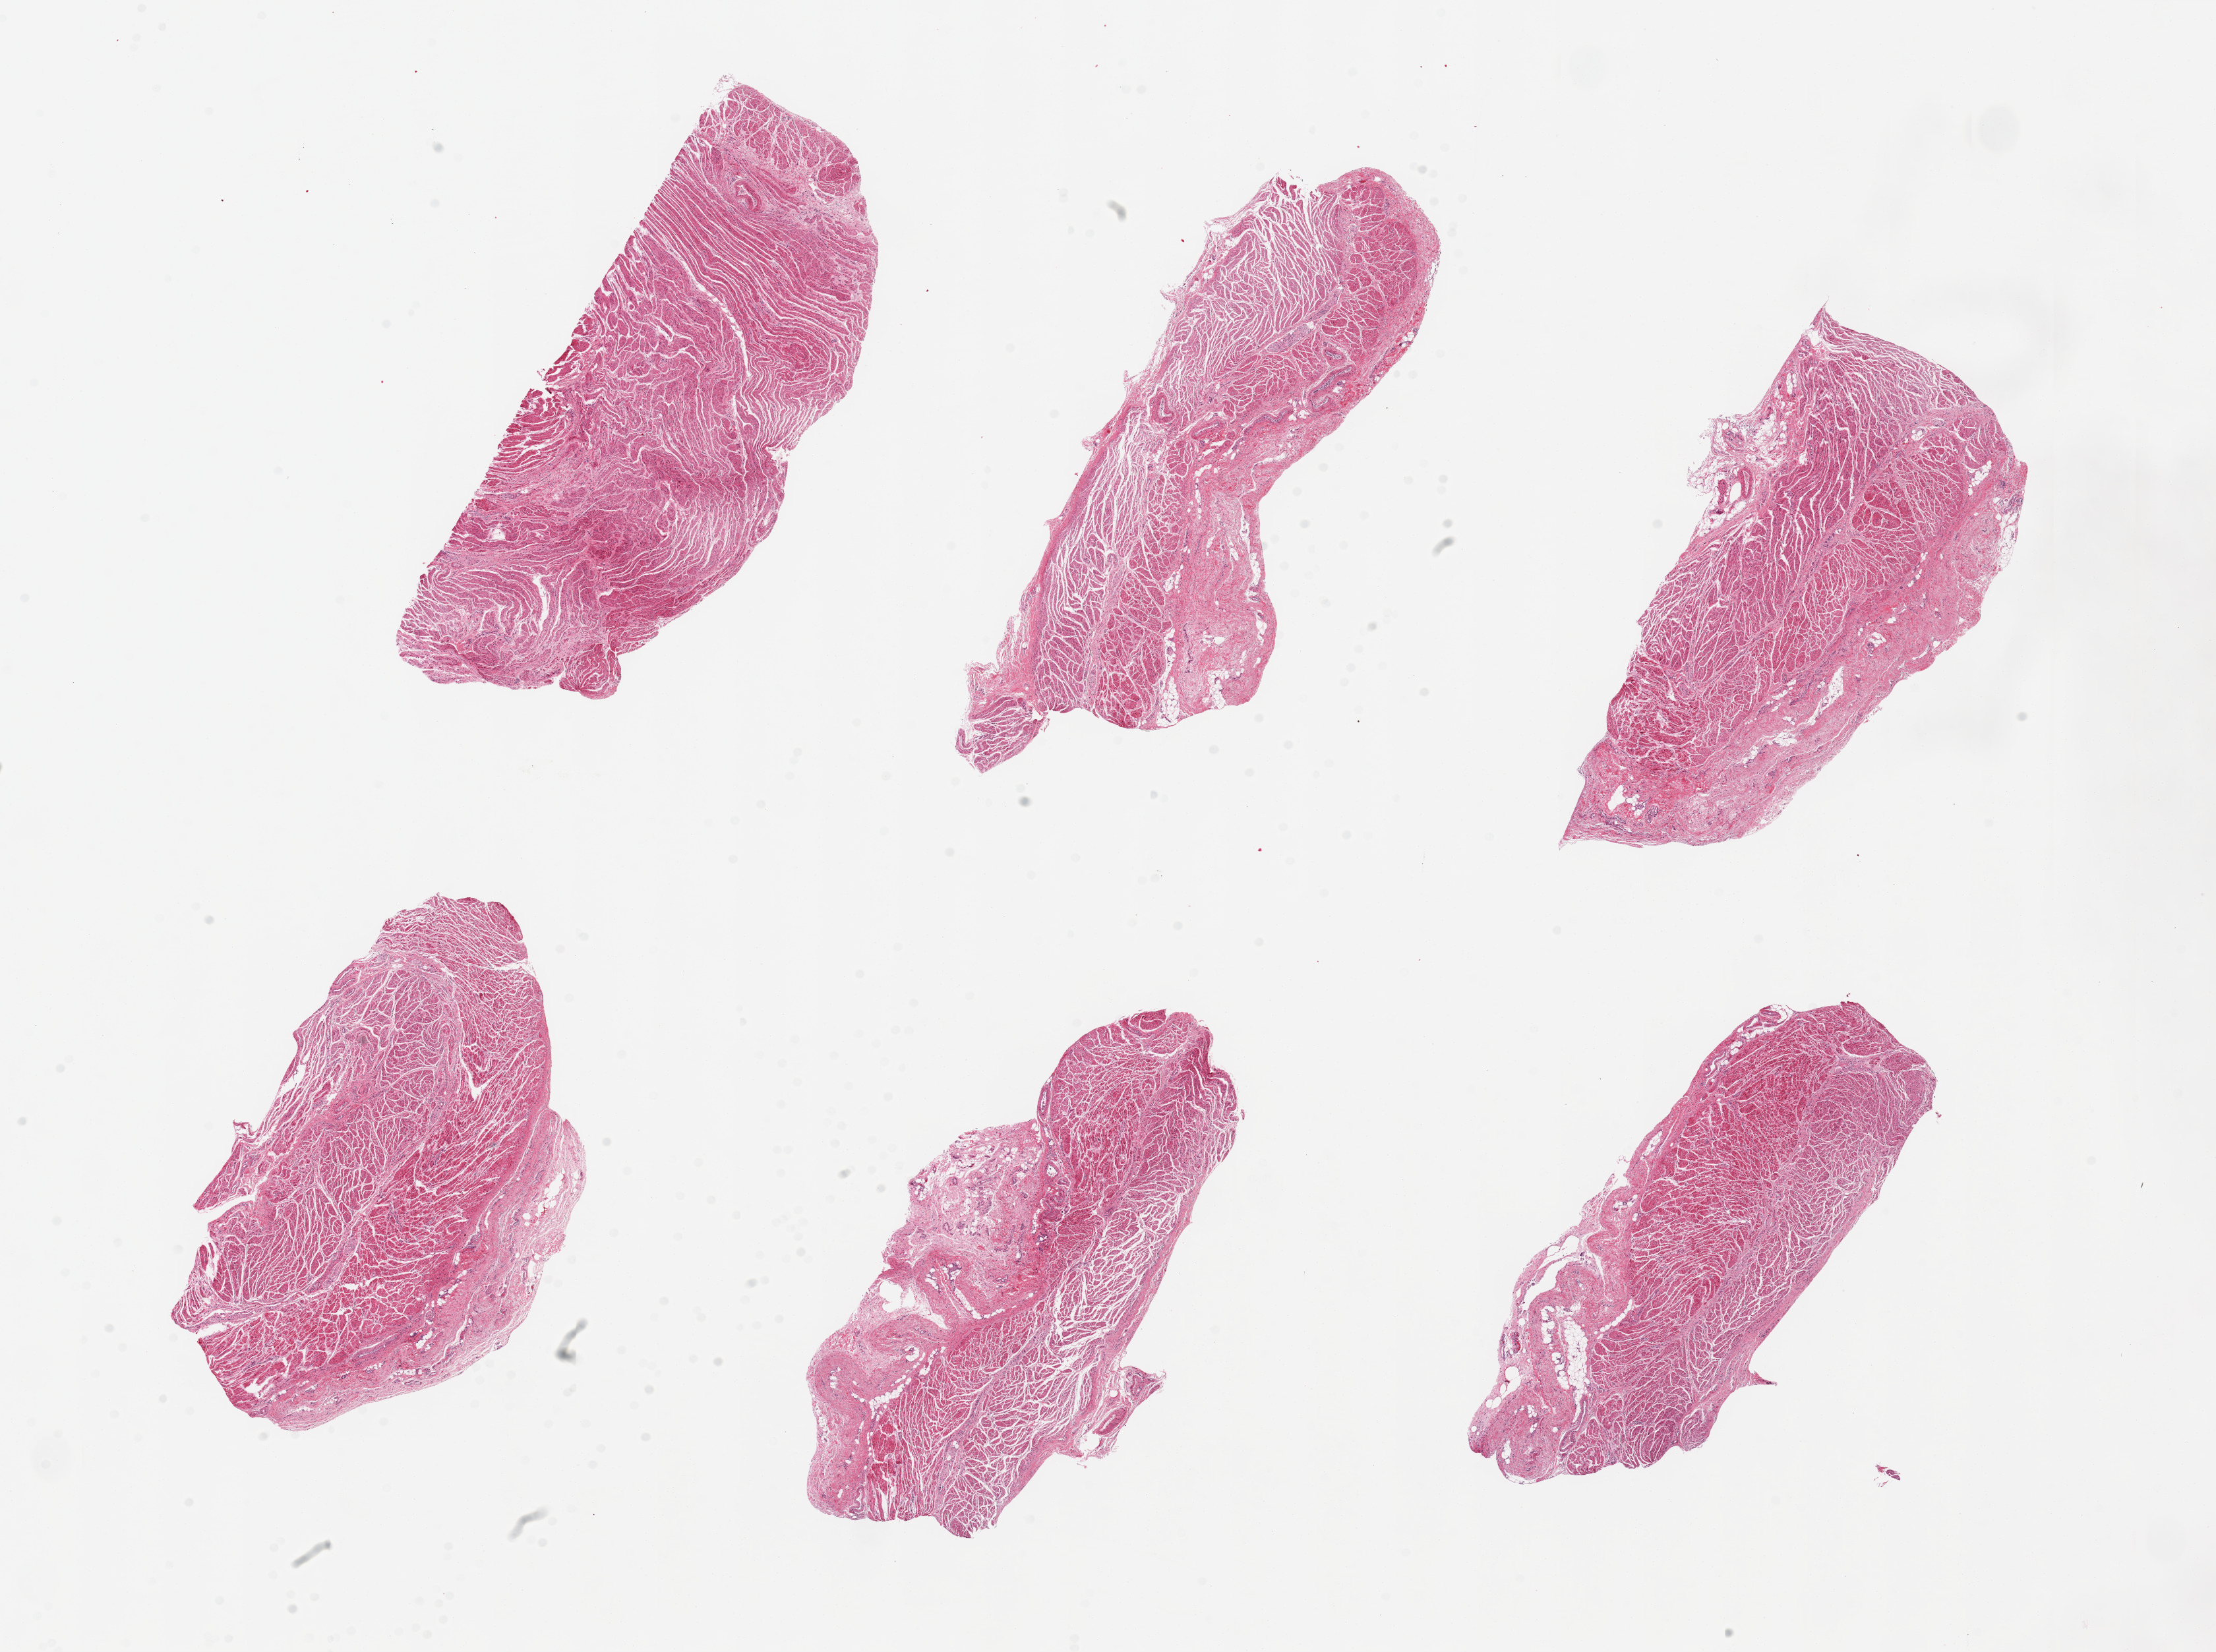
Whole-slide image, hematoxylin and eosin (H&E) stain, brightfield — a low-resolution overview of the entire scanned area, about 26.6 x 19.8 mm, PAXgene-fixed paraffin-embedded (PFPE) section, section of gastroesophageal junction (target tissue), tissue donor sample. Donor: female.
Review note (as recorded): 6 pieces, up to 8x3.5mm; Muscle (target) with prominent fibrous stroma up to 2 mm thick.